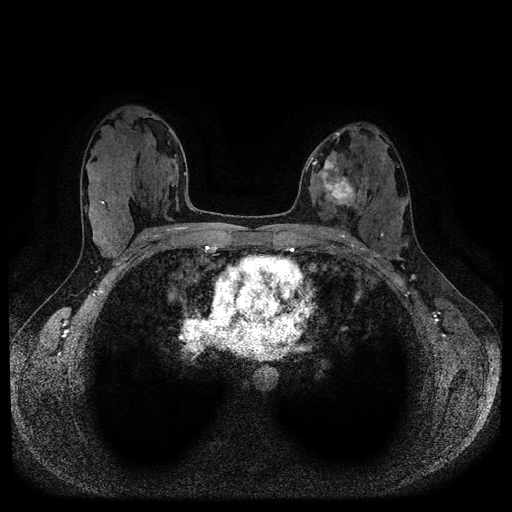
Breast MRI (dynamic contrast-enhanced, multi-phase), one axial slice; position 59 of 116 along the scan axis; dynamic contrast-enhanced series, time point 2 of 5 at this slice position (early post-contrast); 1.5 T; TE 2.6 ms, TR 5.3 ms; 512 × 512 image matrix, field of view 350 × 350 mm. Patient: female, 33 years.
Outlined on this slice (semi-automatically segmented with operator editing):
- breast lesion (labelled 'tumour' in the annotation; benign lesions carry a separate 'benign' label): bounding box <318,157,359,214> (left, top, right, bottom; pixels)